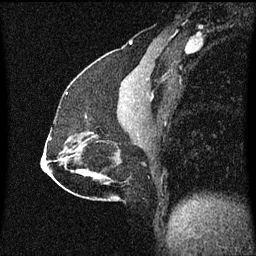
Breast MRI (dynamic contrast-enhanced), one sagittal slice; dynamic contrast-enhanced series, image 2 of 3 at this slice position (ordered by acquisition); 1.5 T; TE 4.2 ms, TR 8.4 ms; 2 mm slice thickness; 256 × 256 image matrix, field of view 200 × 200 mm. Female patient, age 51 years.
Outlined on this slice (semi-automatically segmented with operator editing):
- analysis volume of interest (the breast-tissue region the enhancement analysis was run in; not a lesion): bounding box <80,116,101,139> (left, top, right, bottom; pixels)
- tumour enhancement mask (voxels above the 70 % enhancement threshold inside the analysis volume of interest): <85,116,87,119>